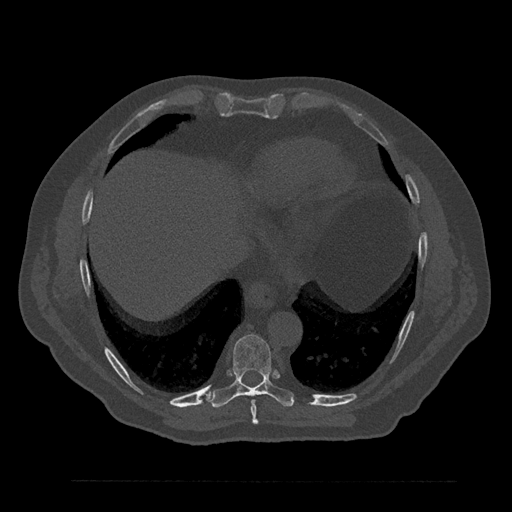
CT including the spine, one axial slice; slice 414 of 797 in the series (ordered by position); 120 kVp; bone window (W 1800 / L 400 HU); 512 × 512 image matrix, field of view 430 × 430 mm. Patient: male, 61 years. From the clinical record (not read from this slice): primary cancer: prostate.
Annotated regions visible in this slice (semi-automatically segmented with operator editing):
- T8 vertebra: bounding box [x1, y1, x2, y2] px = [251, 400, 258, 425]
- T9 vertebra: [208, 334, 295, 408]